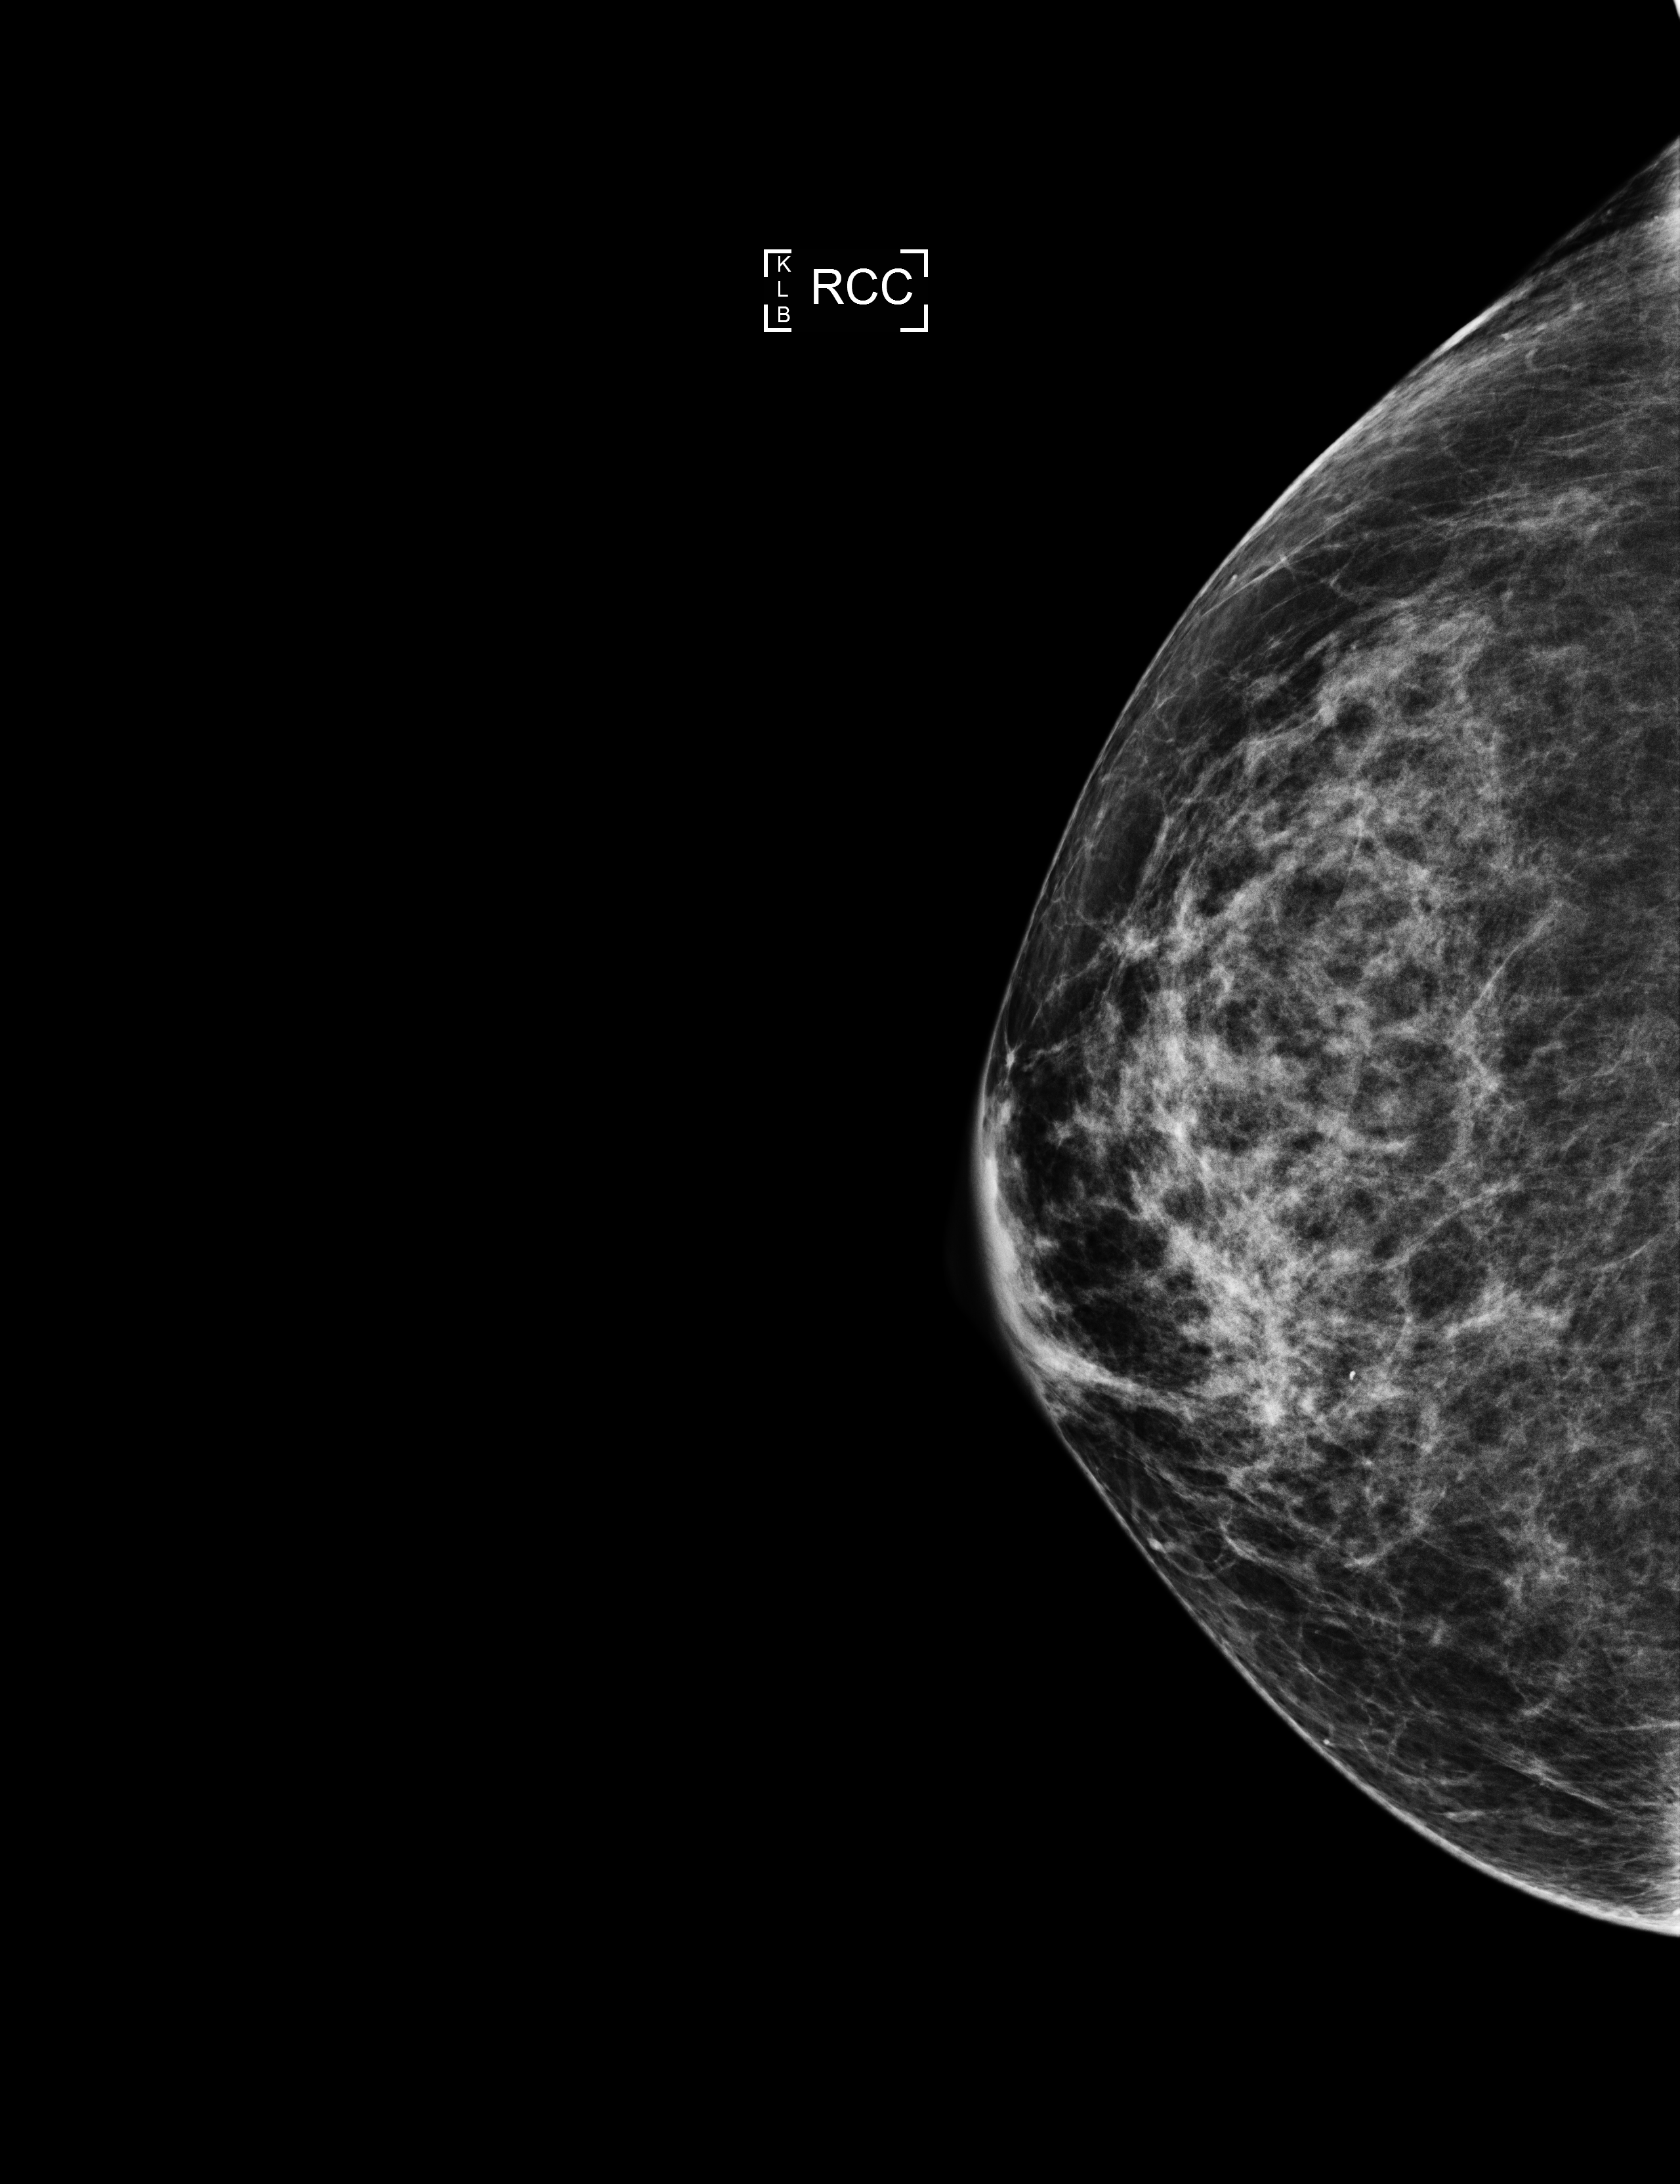
Annual screening mammography examination; compressed breast thickness 63 mm. Female patient, age 64 years.
Image type: full-field digital mammogram. Breast: right. Projection: CC view.